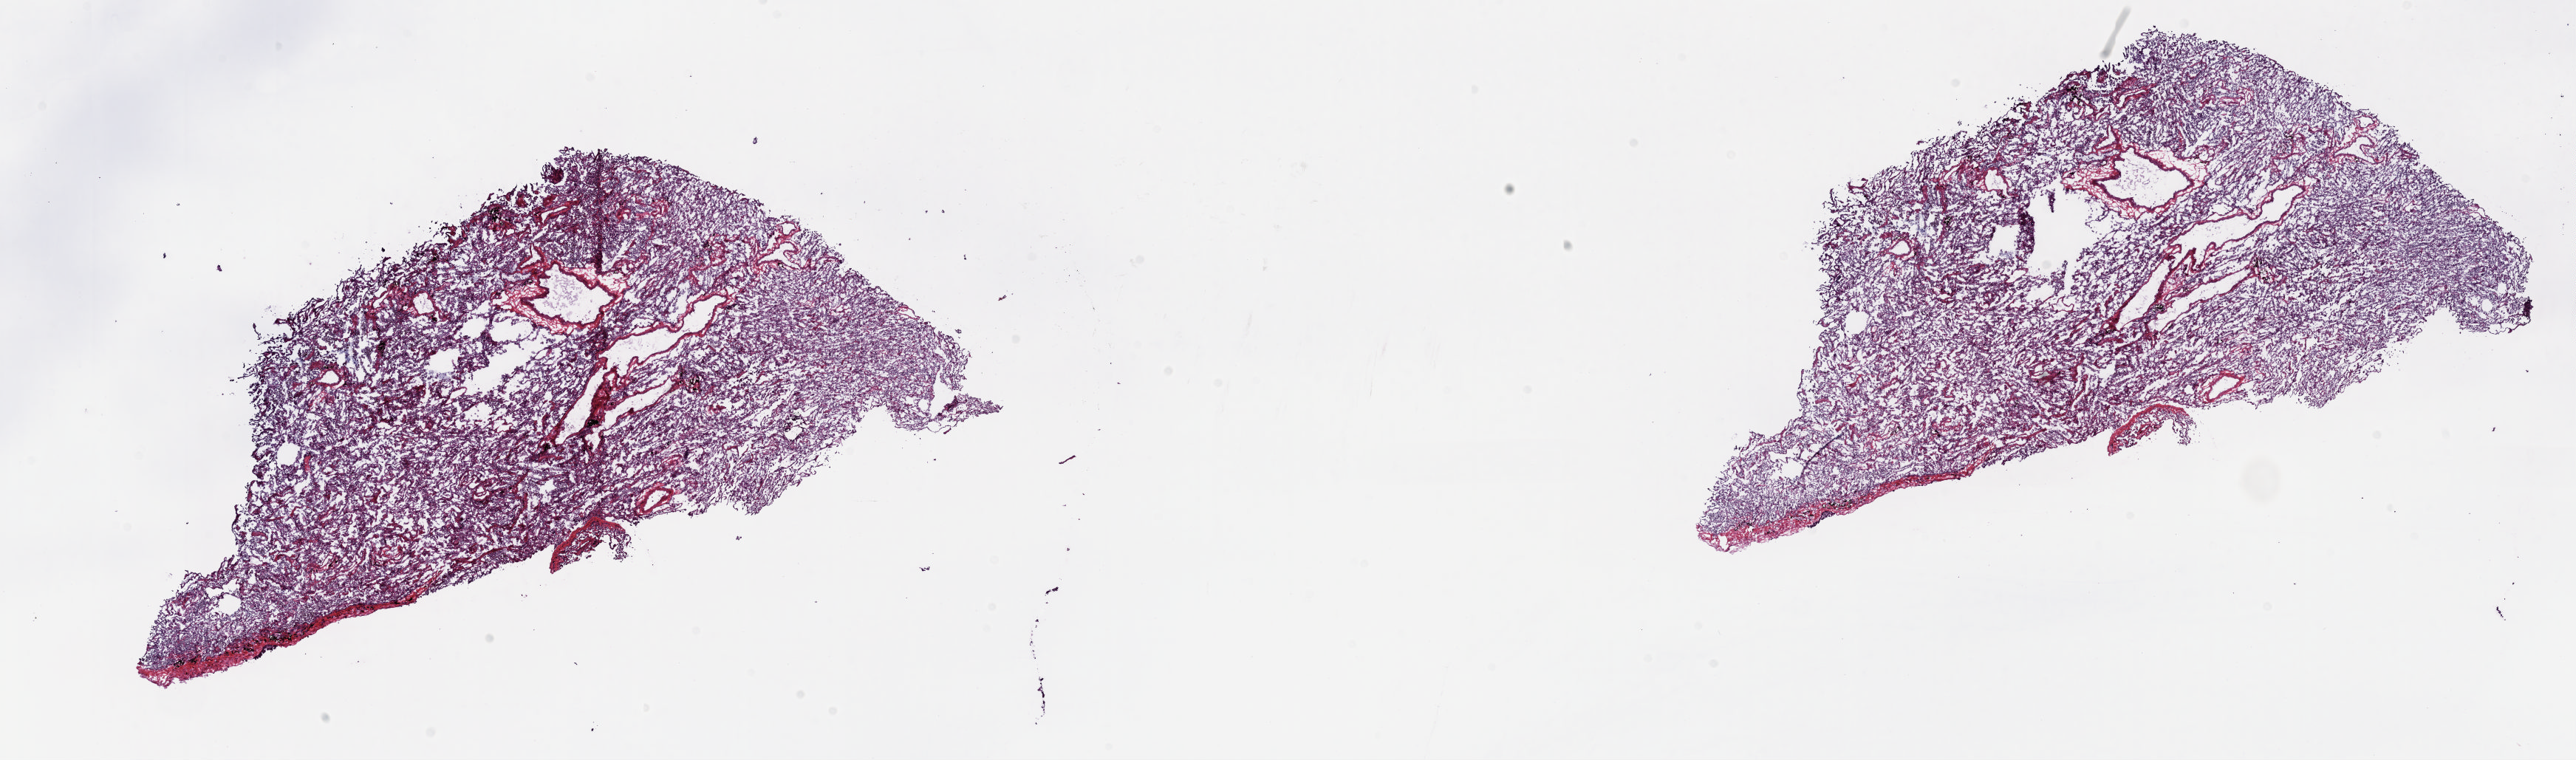
Digitized H&E tissue section (whole slide) — whole scanned area (about 28.1 x 8.3 mm, slide scanned at 20x) shown as a low-resolution overview. Frozen section from the top of the tissue portion. Solid tissue normal (non-tumour tissue) sample from the lung. Patient: female, age at initial diagnosis 39 years. Composition of this section per pathologist review: tumour cells 0%, tumour nuclei 0%, normal cells 50%, stromal cells 50%, necrosis 0%. Infiltration values recorded for this section: lymphocyte infiltration 3%, monocyte infiltration 20%, neutrophil infiltration 2%.
• this section: solid tissue normal (non-tumour) sample from the same patient
• patient diagnosis: Papillary adenocarcinoma, NOS